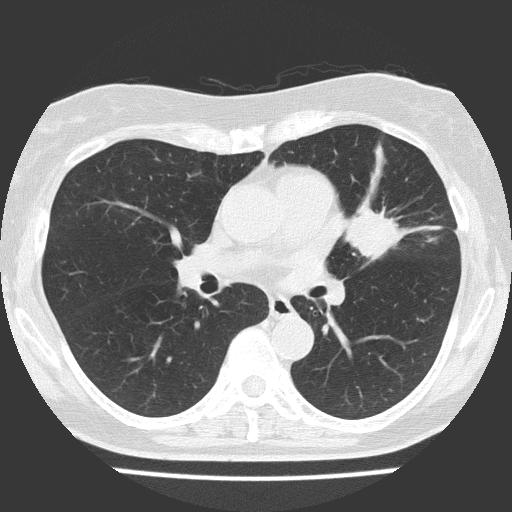
Axial slice from a low-dose chest CT screening exam. First (baseline) screen. Lung window (W 1500 / L -600 HU). Slice 71 of 151 in the series. Female, age 70 years at enrolment. Current smoker at enrolment.
Expert reader's lesion annotation, bounding box (x1, y1, x2, y2) in pixels: (322, 181, 432, 275). The screening reader recorded 2 non-calcified nodules or masses ≥4 mm on this exam (left upper lobe, right upper lobe); which of them this box marks is not recorded. Later outcome: lung cancer diagnosed 25 days after this screen — adenocarcinoma, NOS, left upper lobe, poorly differentiated (G3), stage IV (AJCC 6th edition), 30 mm at pathology.